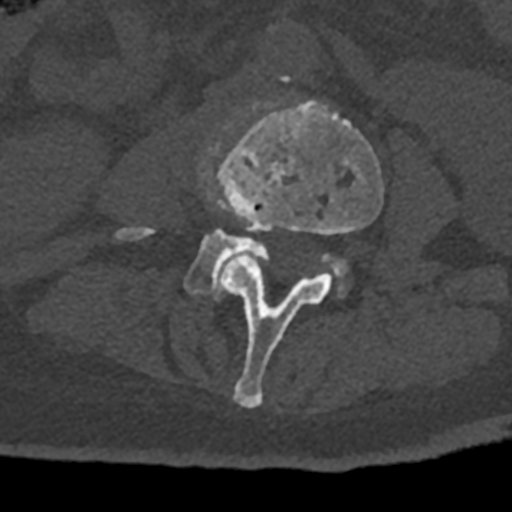
CT including the spine, one axial slice; position 297 of 797 along the scan axis; bone window (W 1800 / L 400 HU); 0.5 mm slice thickness; 512 × 512 image matrix. Male patient, age 74 years. From the clinical record (not read from this slice): primary cancer: renal.
Structures marked on this image (semi-automatically segmented with operator editing):
- L3 vertebra: bounding box (x1, y1, x2, y2) in pixels: (216, 101, 383, 408)
- L4 vertebra: (116, 145, 348, 300)